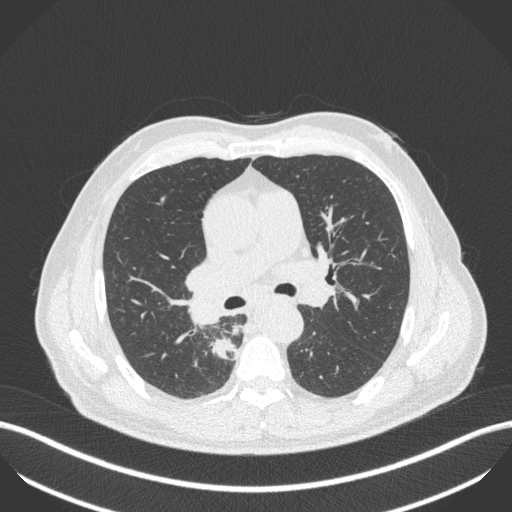
Chest CT, one axial slice. Slice 279 of 451 in the series (ordered by position). Reconstruction kernel B31f. 100 kVp. Lung window (W 1500 / L -600 HU). 1 mm slice thickness. 512 × 512 image matrix. Male patient, age 61 years. From the clinical record (not read from this slice): clinical TNM (as recorded): T1 N0 M0; histopathological grade: G3.
Outlined on this slice (bounding box drawn by a radiologist):
- lung tumour (recorded histology: small cell carcinoma): bounding box (x1, y1, x2, y2) in pixels: (206, 332, 242, 372)